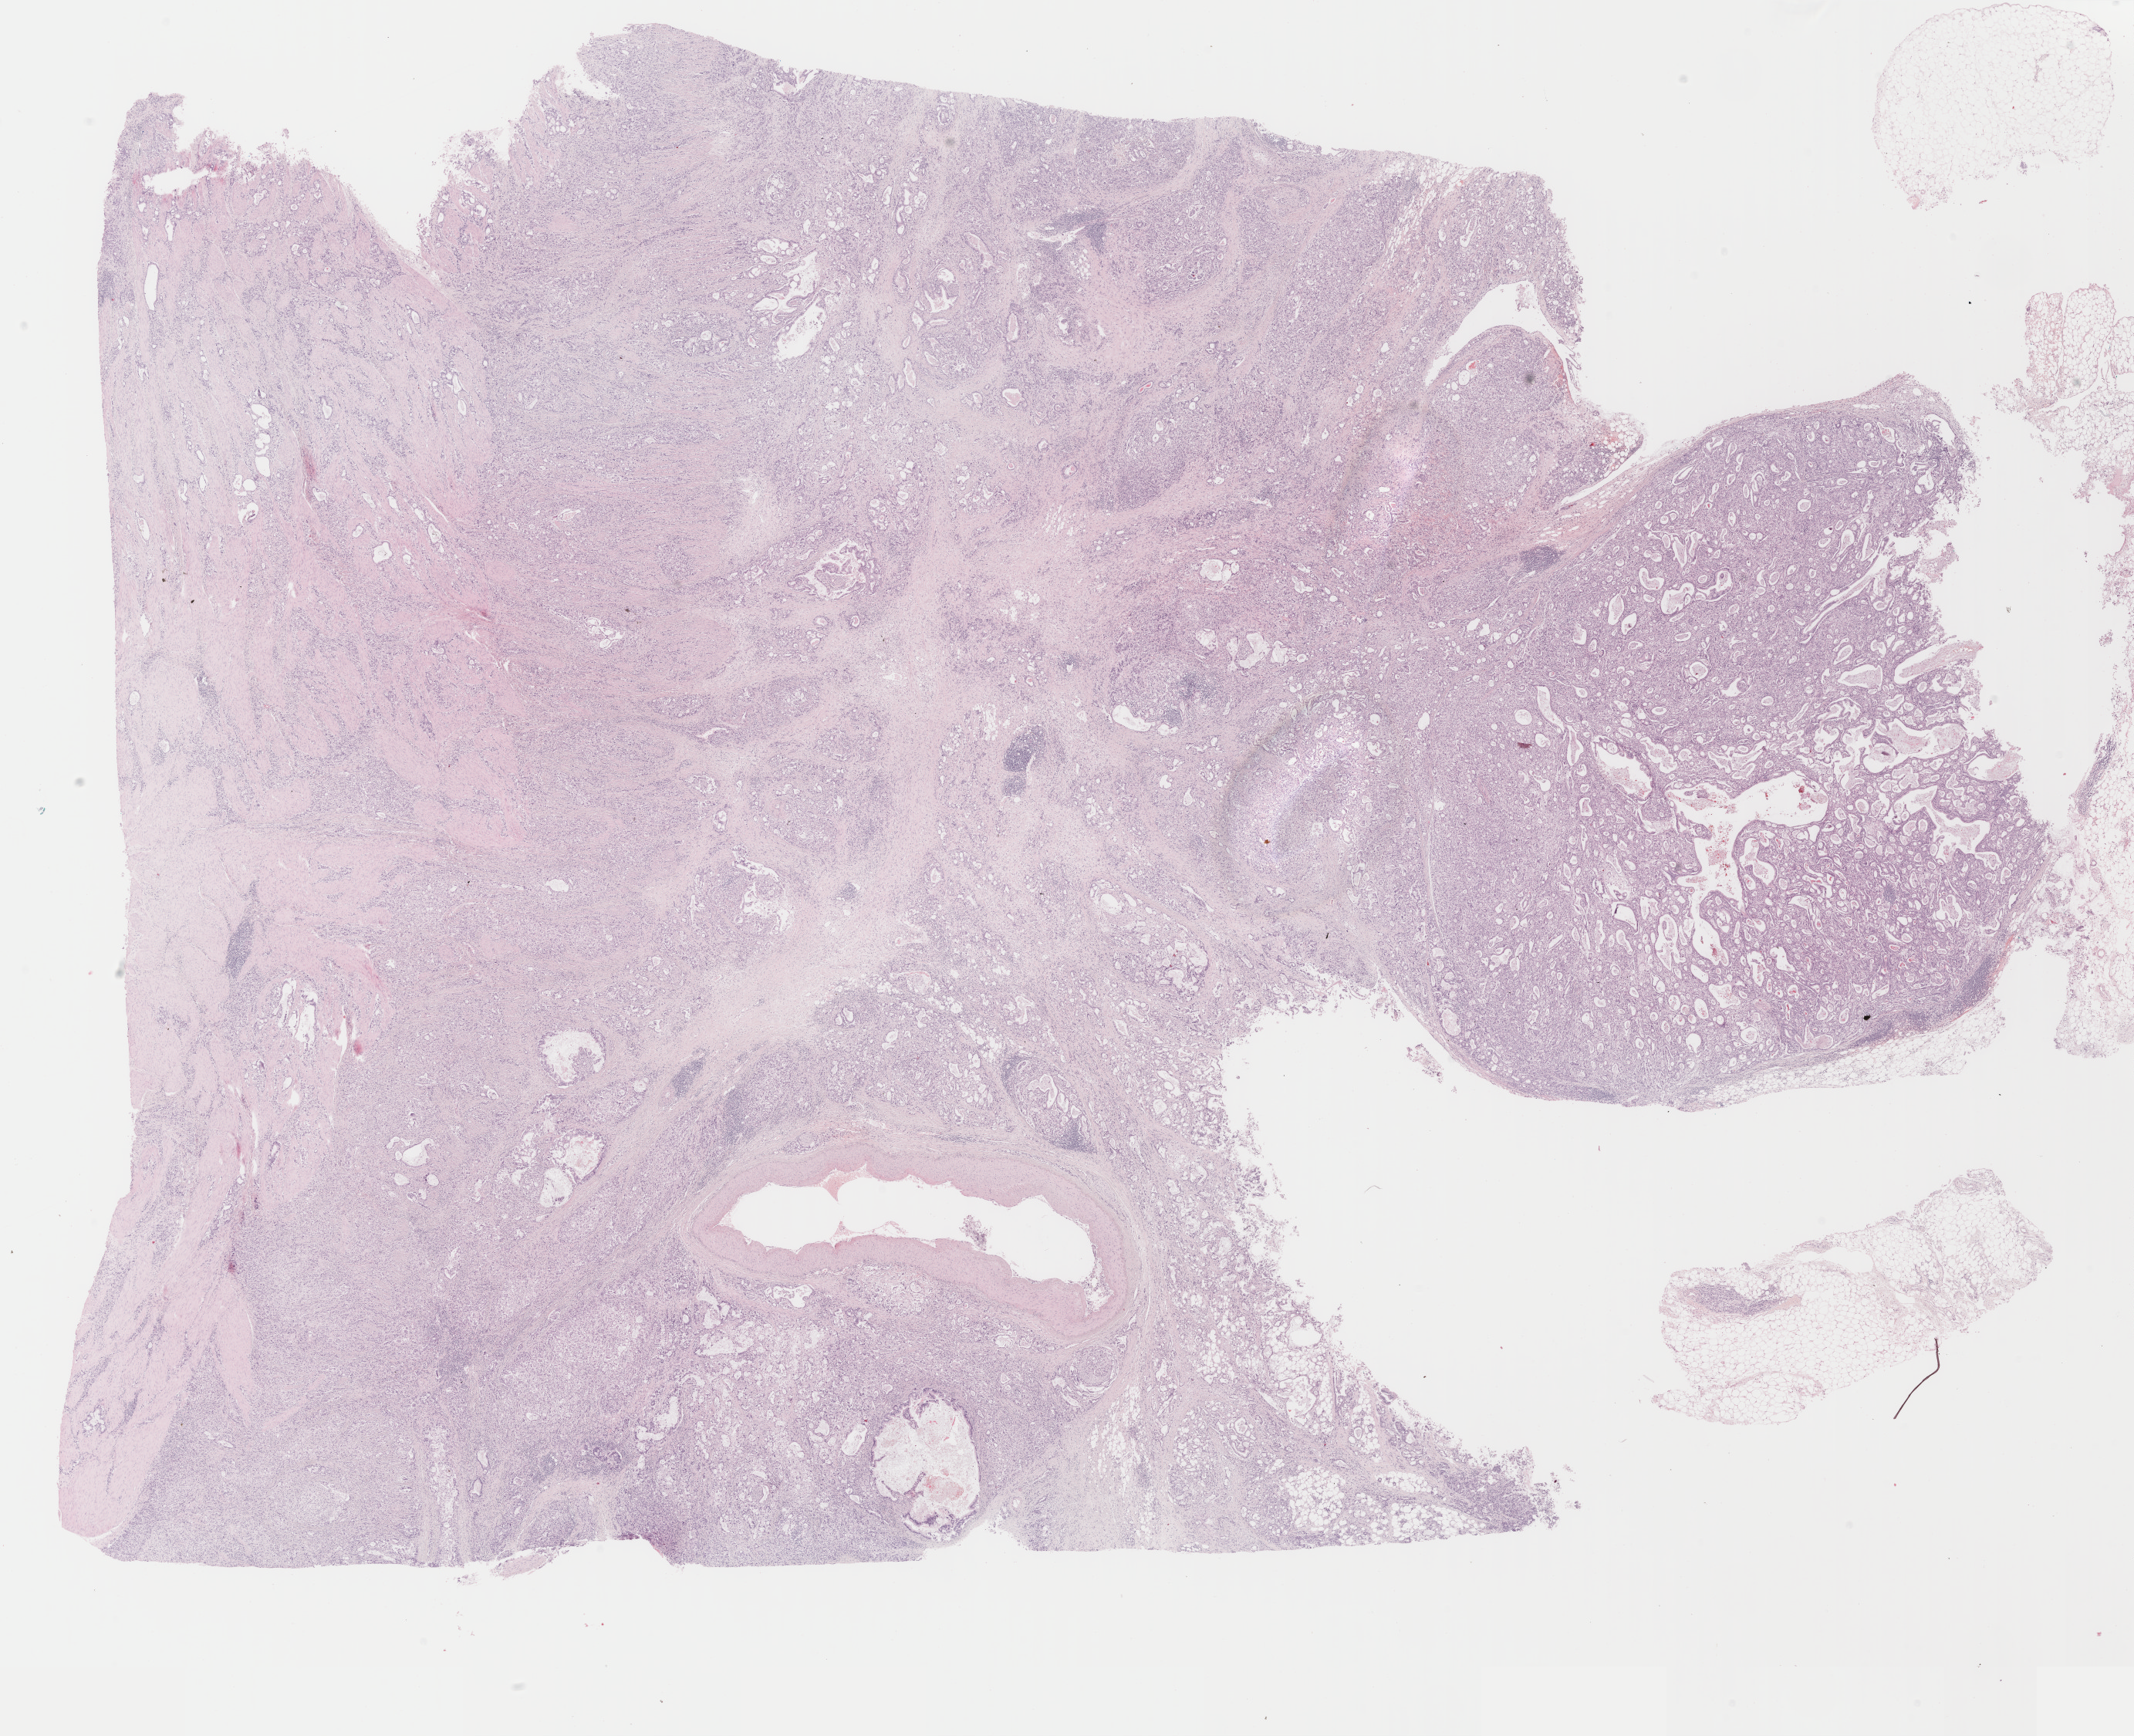
Digitized Hematoxylin and eosin (H&E) stained tissue section (whole slide), whole scanned area (about 22.0 x 17.9 mm) shown as a low-resolution overview. Formalin-fixed paraffin-embedded (FFPE) diagnostic section. Sample: primary tumour, stomach. Male, age 75 years at initial diagnosis. Histologic grade: G3 (poorly differentiated).
- AJCC pathologic stage: IIIA (7th edition)
- diagnosis: Tubular adenocarcinoma (fundus of stomach)